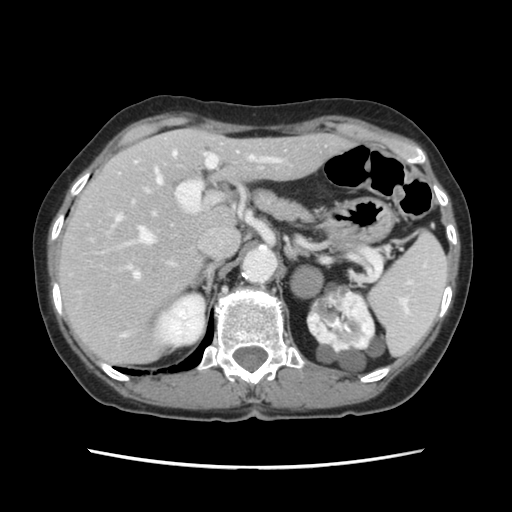
Contrast-enhanced abdominal CT, one axial slice. Slice 82 of 120 in the series (ordered by position). 120 kVp. Intravenous contrast given. Soft-tissue window (W 400 / L 40 HU). 2.5 mm slice thickness. 512 × 512 image matrix, field of view 330 × 330 mm. Female patient, age 70 years. Case-level facts recorded for this patient, not image findings: diagnosis: colorectal cancer liver metastases, imaged before liver resection; multiple liver metastases: no; largest metastasis: 2.5 cm; disease in both lobes: no.
Annotated regions visible in this slice (expert manual segmentation):
- hepatic veins: bounding box (x1, y1, x2, y2) in pixels: (139, 152, 177, 244)
- liver: (59, 129, 343, 363)
- planned liver remnant (the part of the liver to remain after resection): (100, 129, 343, 288)
- portal vein (with intrahepatic branches): (115, 153, 282, 279)